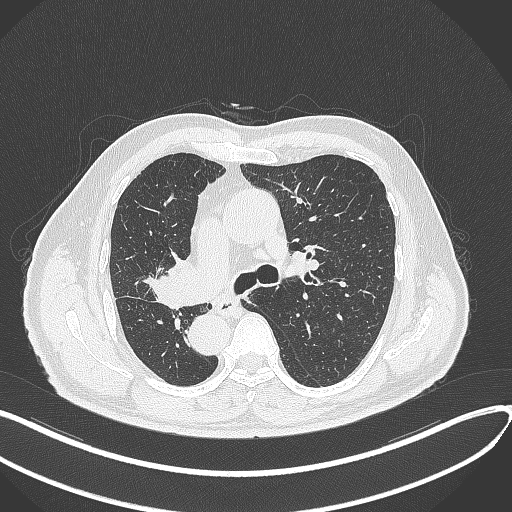
Chest CT, one axial slice; slice 190 of 300 in the series (ordered by position); reconstruction kernel B70f; 120 kVp; lung window (W 1500 / L -600 HU); 1 mm slice thickness; 512 × 512 image matrix, field of view 400 × 400 mm. Patient: male, 67 years. From the clinical record (not read from this slice): clinical TNM (as recorded): T2a N0 M0.
Outlined on this slice (bounding box drawn by a radiologist):
- lung tumour (recorded histology: squamous cell carcinoma): bounding box (x1, y1, x2, y2) in pixels: (141, 253, 205, 312)